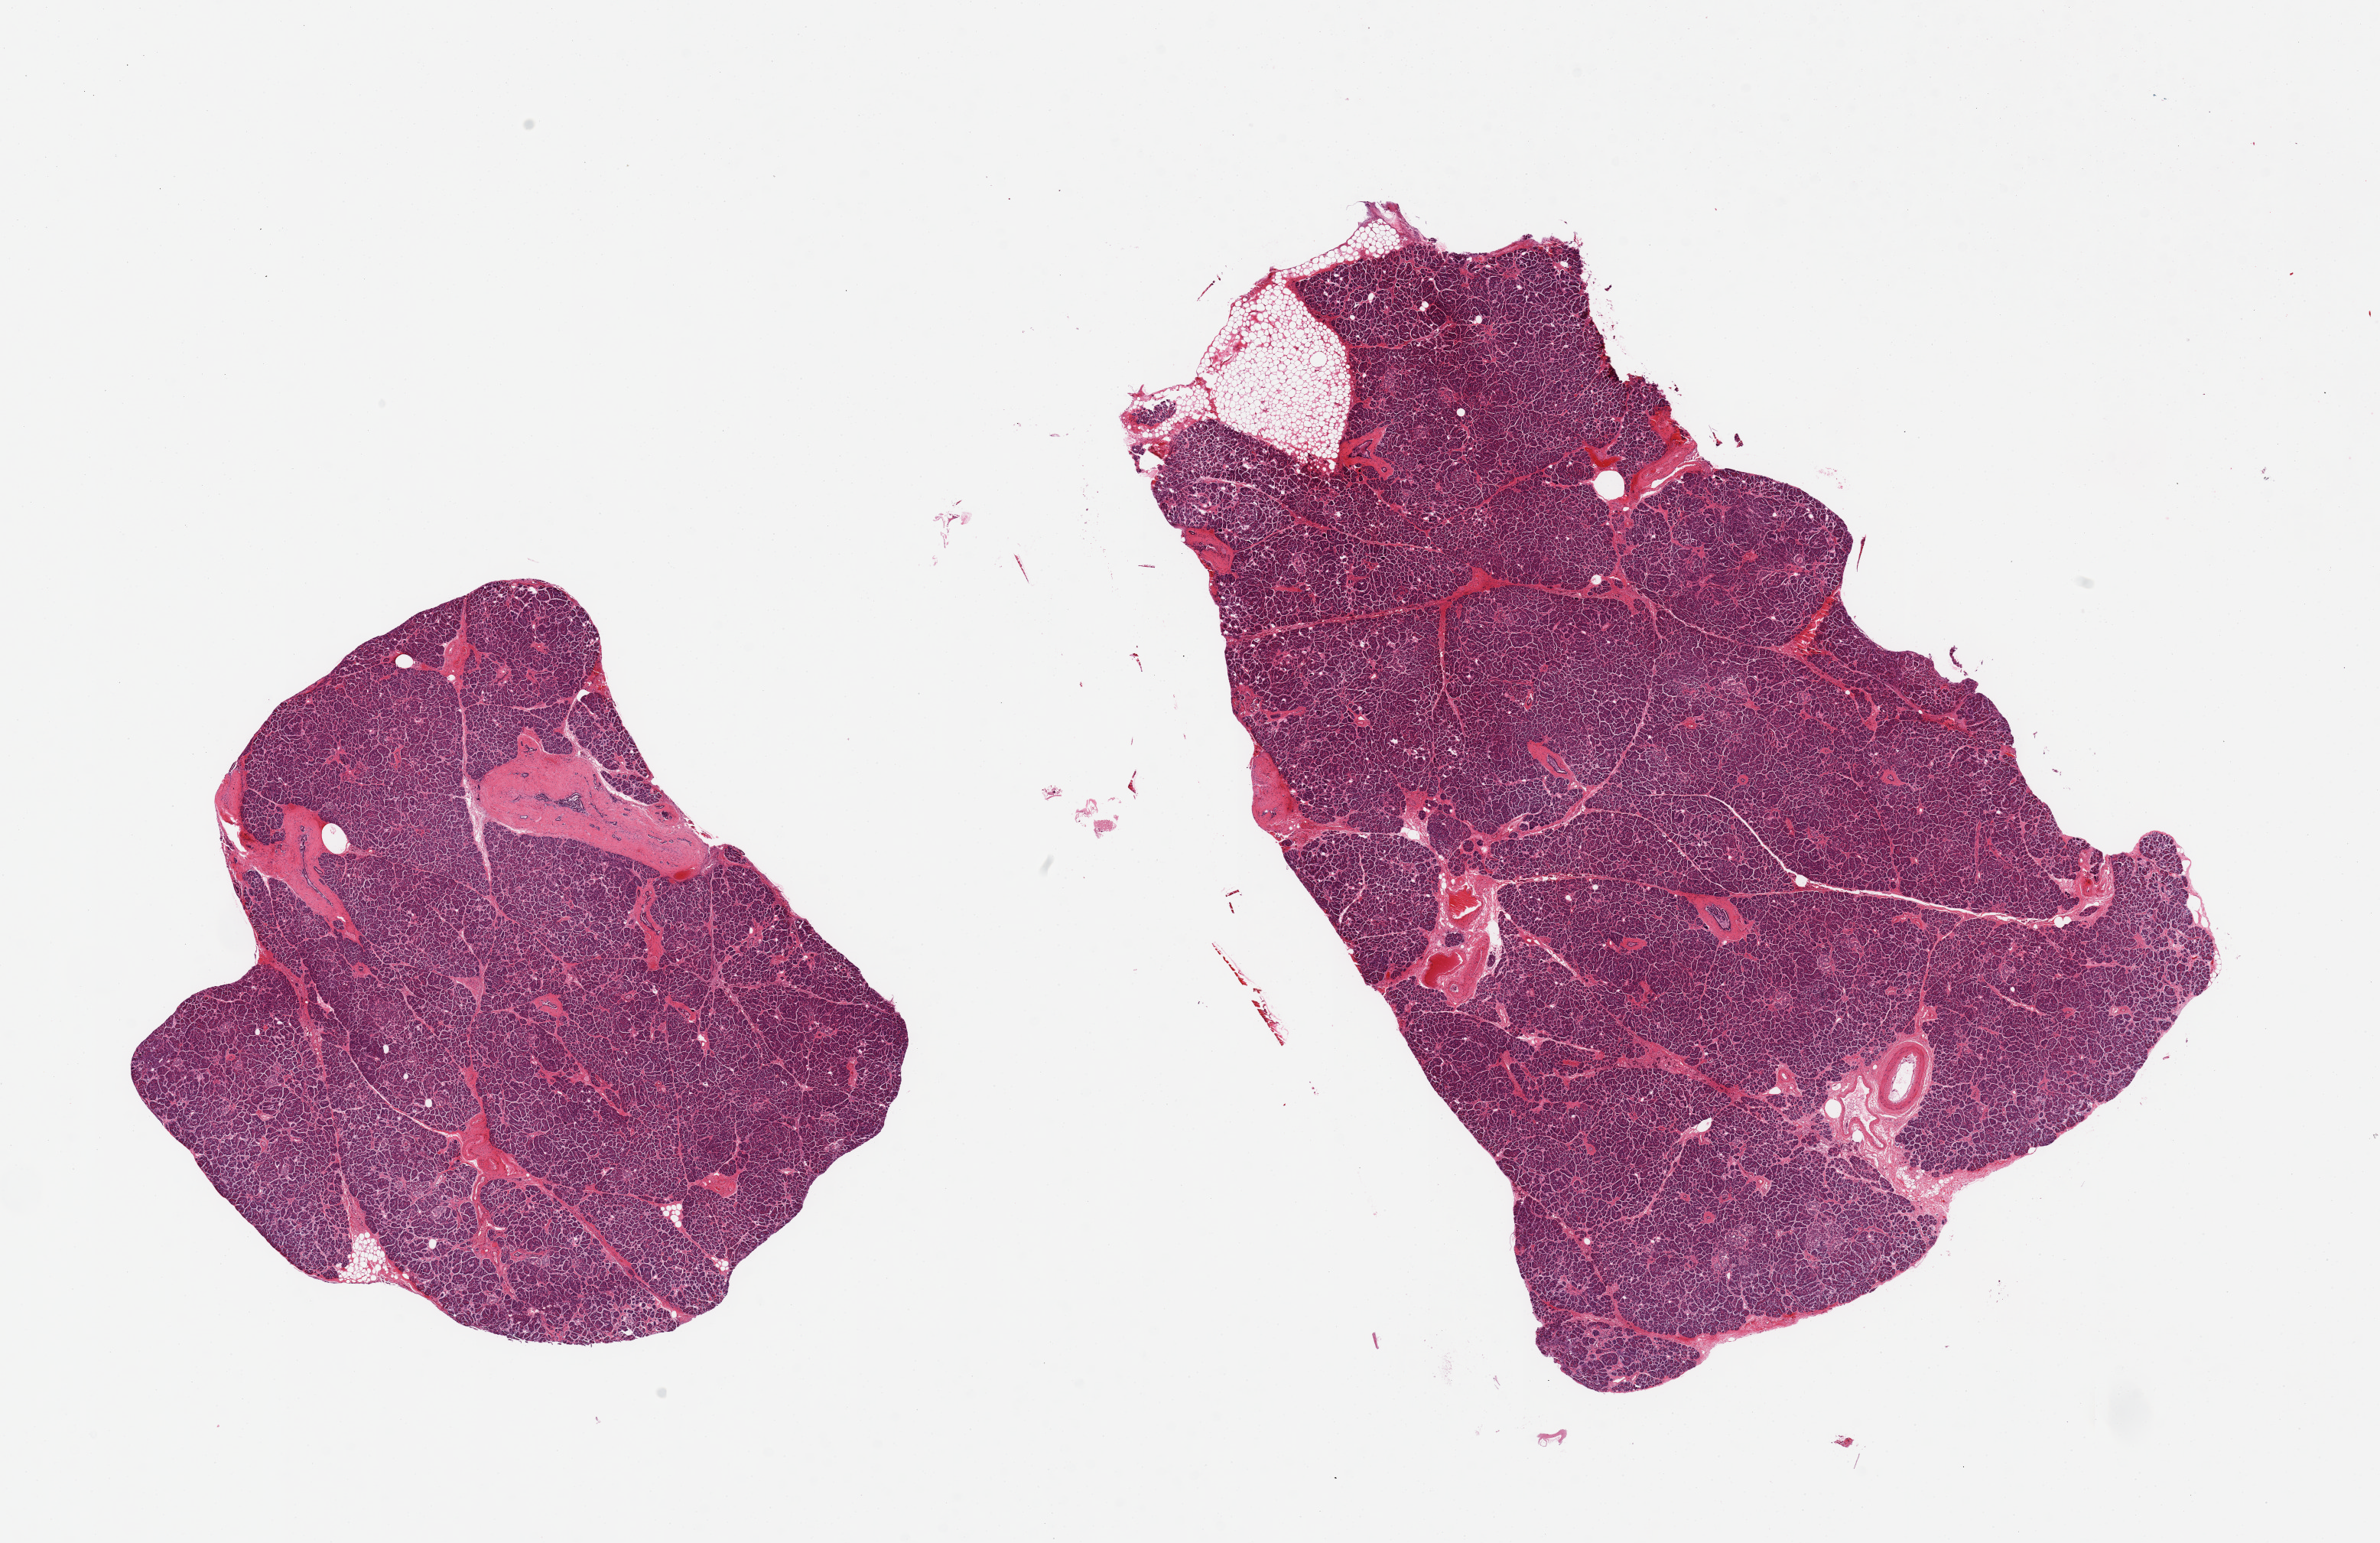
Digitized haematoxylin and eosin-stained section, a low-resolution overview of the entire scanned area, about 24.6 x 16.0 mm (acquisition: 20x scan); PAXgene-fixed, paraffin-embedded tissue; target tissue: pancreas; tissue donor sample. Donor sex: male.
Reviewer comment on this tissue sample: 2 pieces, approaching score '2' for autolysis; Islets still visible, early saponification present.